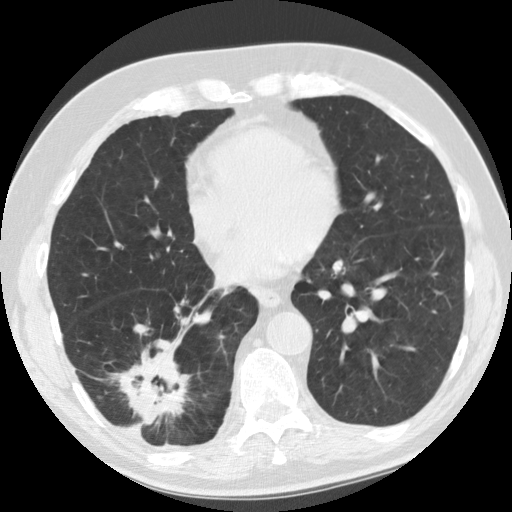
Low-dose screening chest CT, axial slice; baseline screening round; lung window (W 1500 / L -600 HU); 2.5 mm slice thickness; slice 88 of 135 in the series. Male participant, aged 69 years at enrolment. Former smoker at enrolment.
Expert reader's lesion annotation, box from (x=108, y=332) to (x=194, y=441) px. The screening reader recorded 2 non-calcified nodules or masses ≥4 mm on this exam (right lower lobe, right lower lobe); which of them this box marks is not recorded.